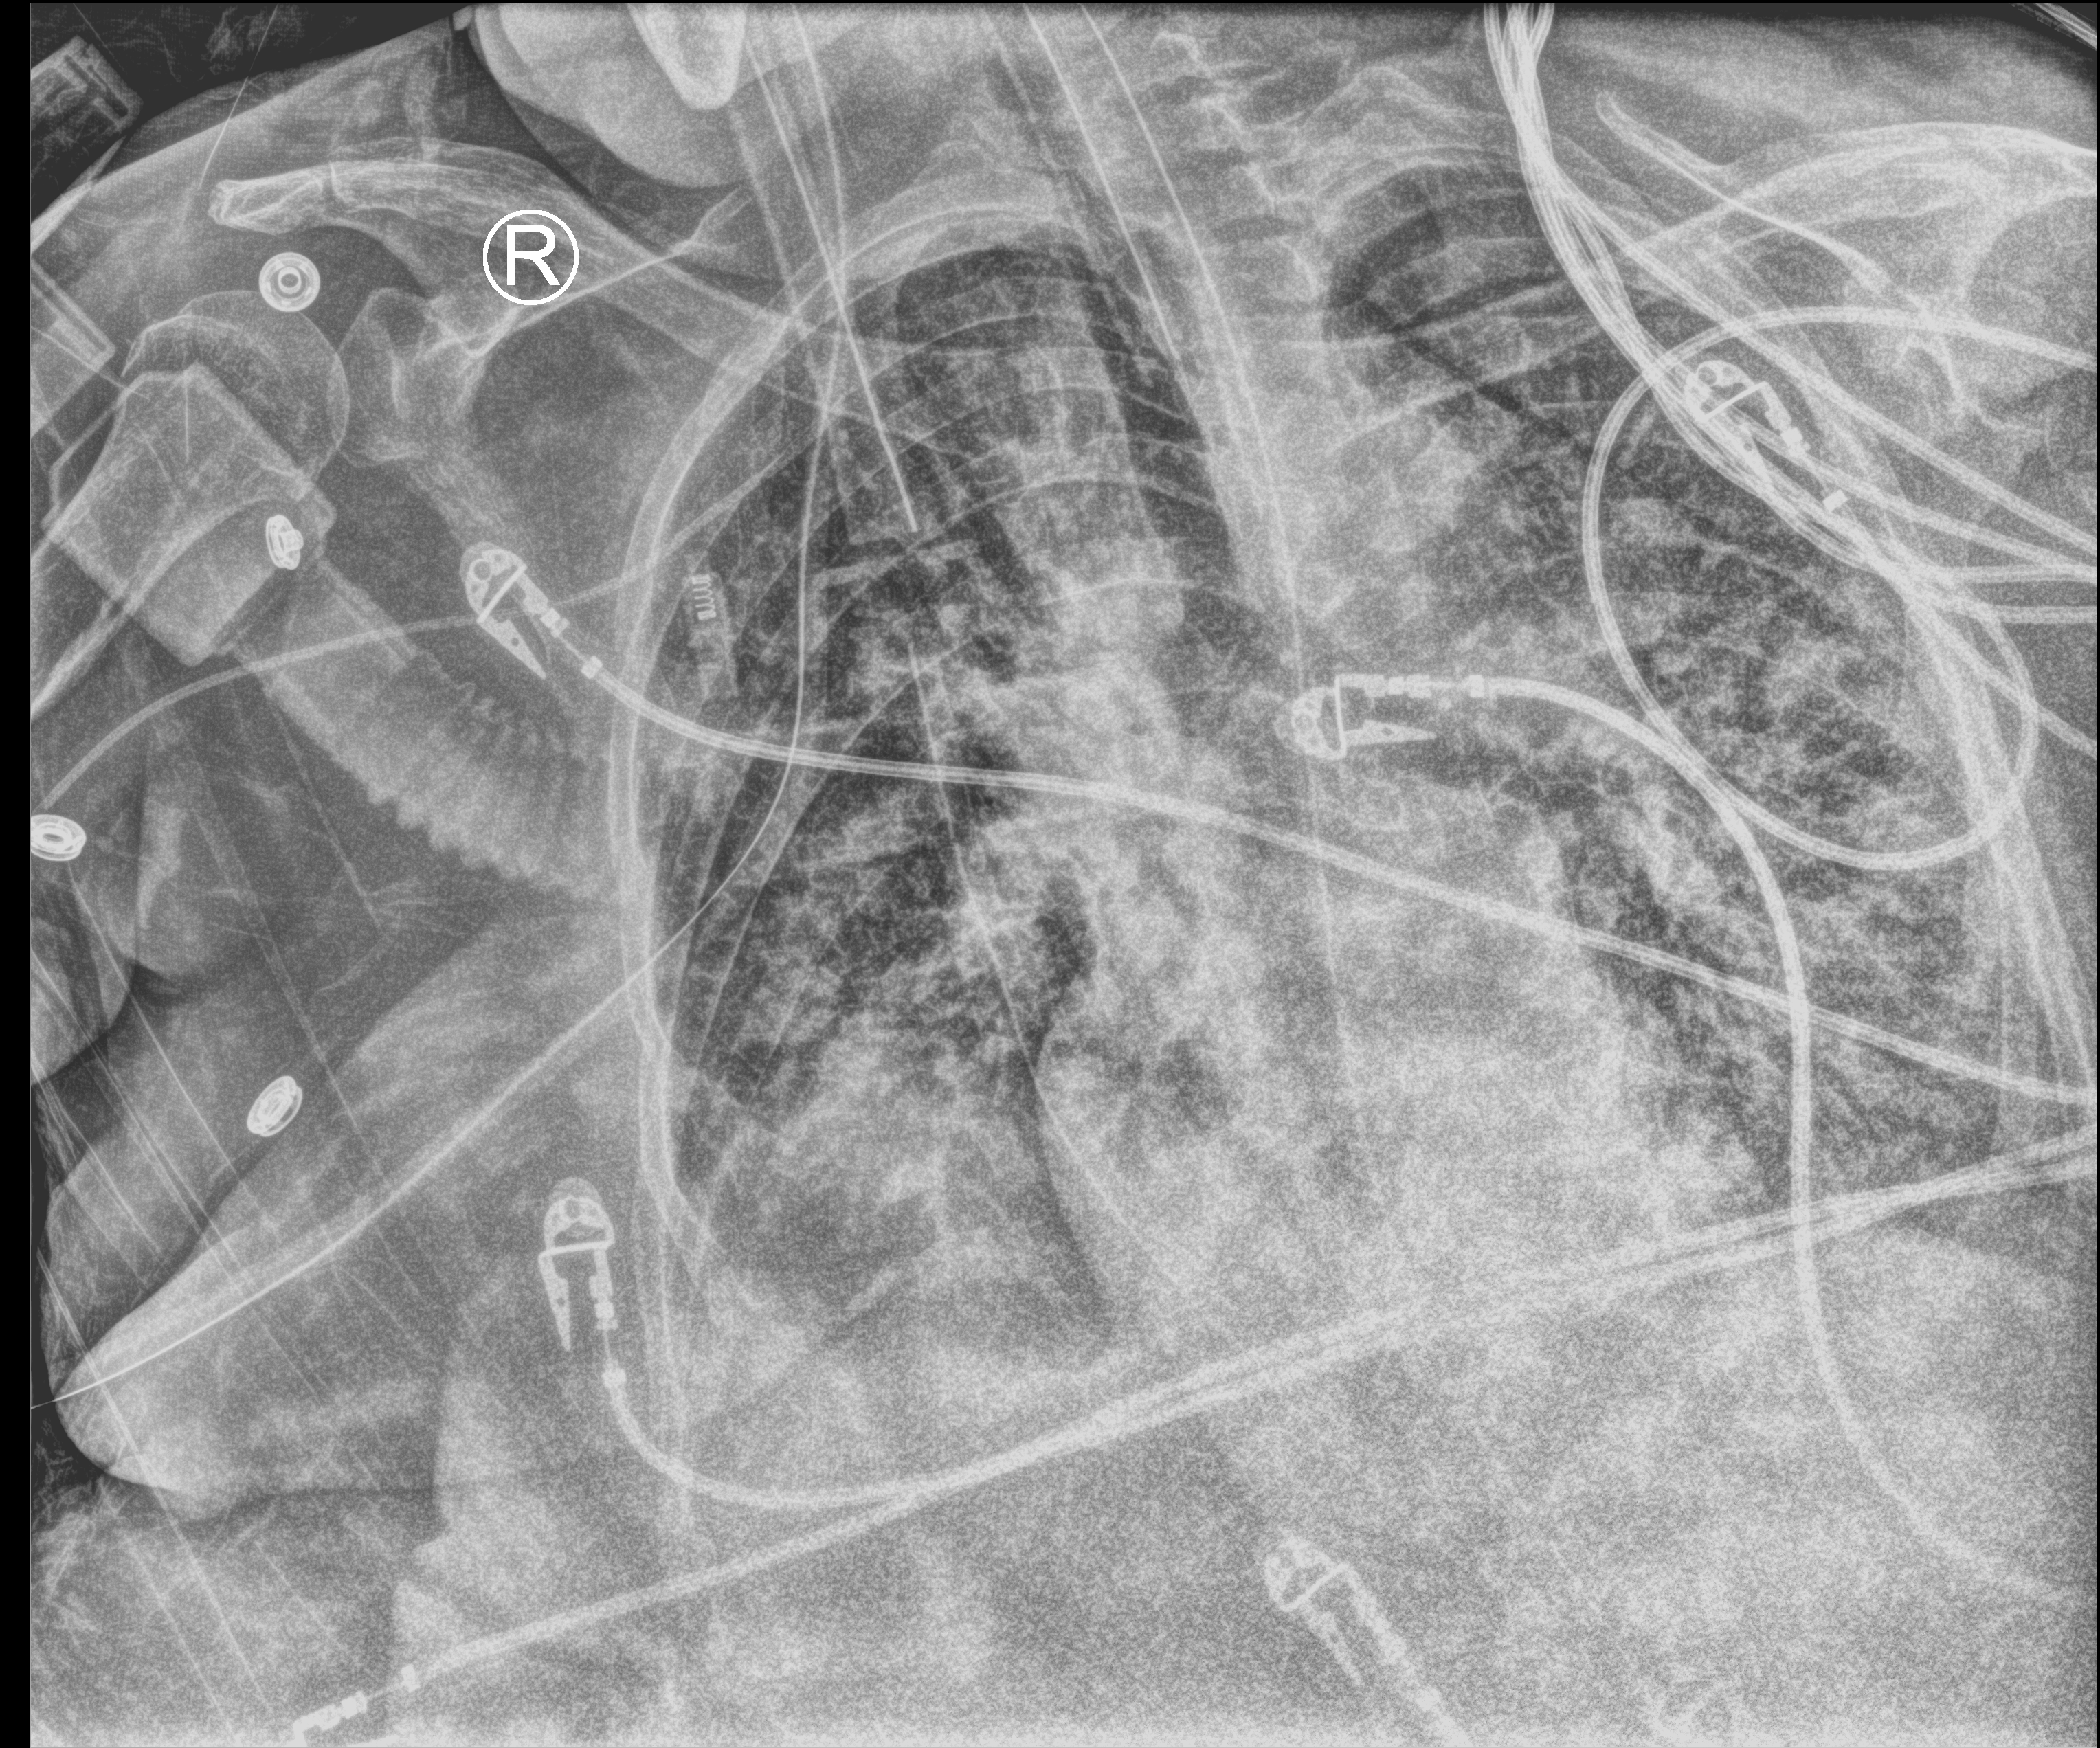
Portable chest radiograph; anteroposterior (AP) projection. Female patient hospitalised with COVID-19, age 60–74 years.
Hospital-stay facts (about this admission, not read from this image; timing relative to this image not recorded): hypertension (admission record): yes; mechanically ventilated during this hospital stay: yes.